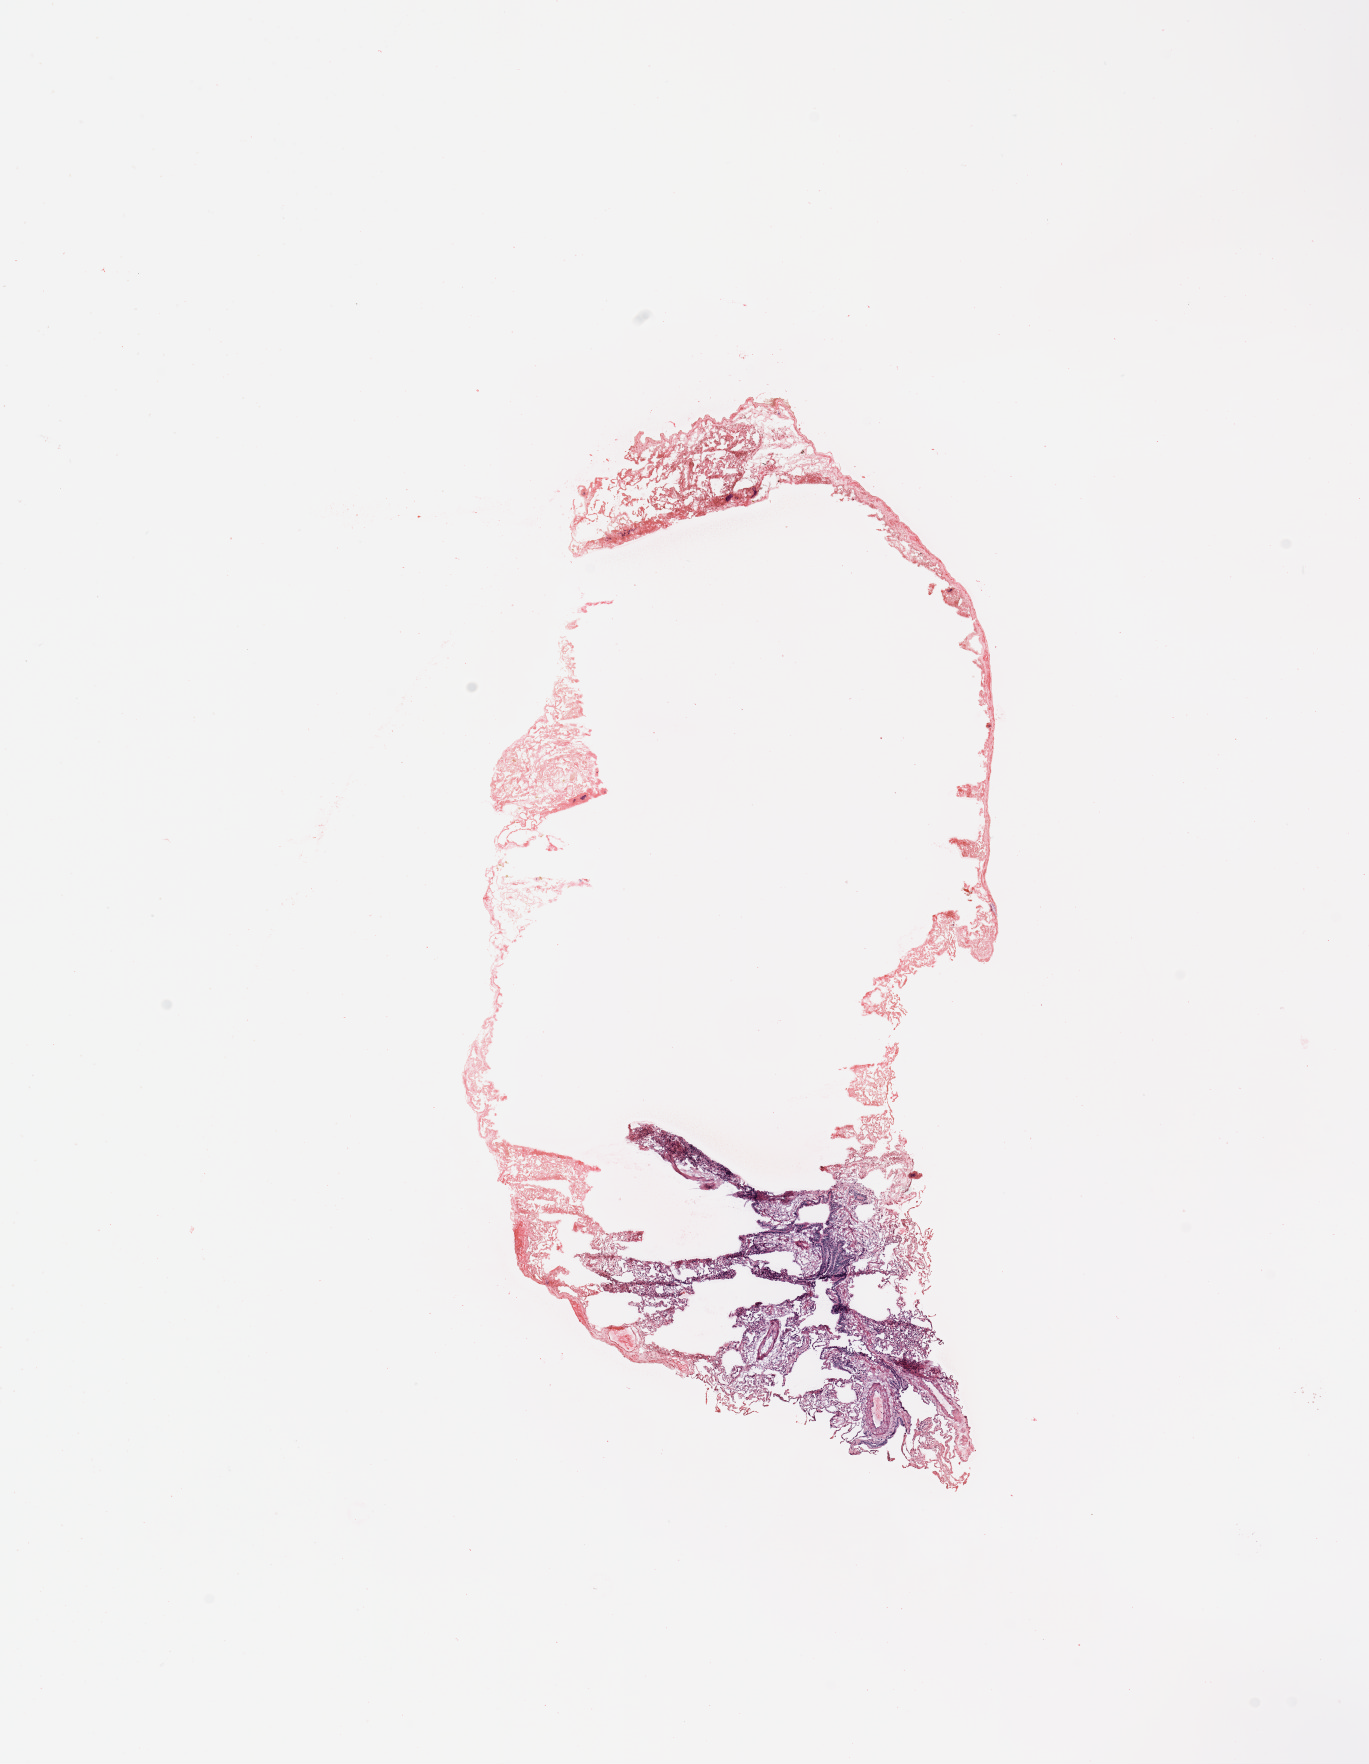
H&E-stained whole-slide image, whole scanned area (about 10.8 x 14.0 mm) shown as a low-resolution overview, normal (non-tumour) tissue sample, sampled site: lung. Male, 79 y/o.
* this section: normal (non-tumour) tissue from the same patient
* patient diagnosis: Adenocarcinoma, NOS